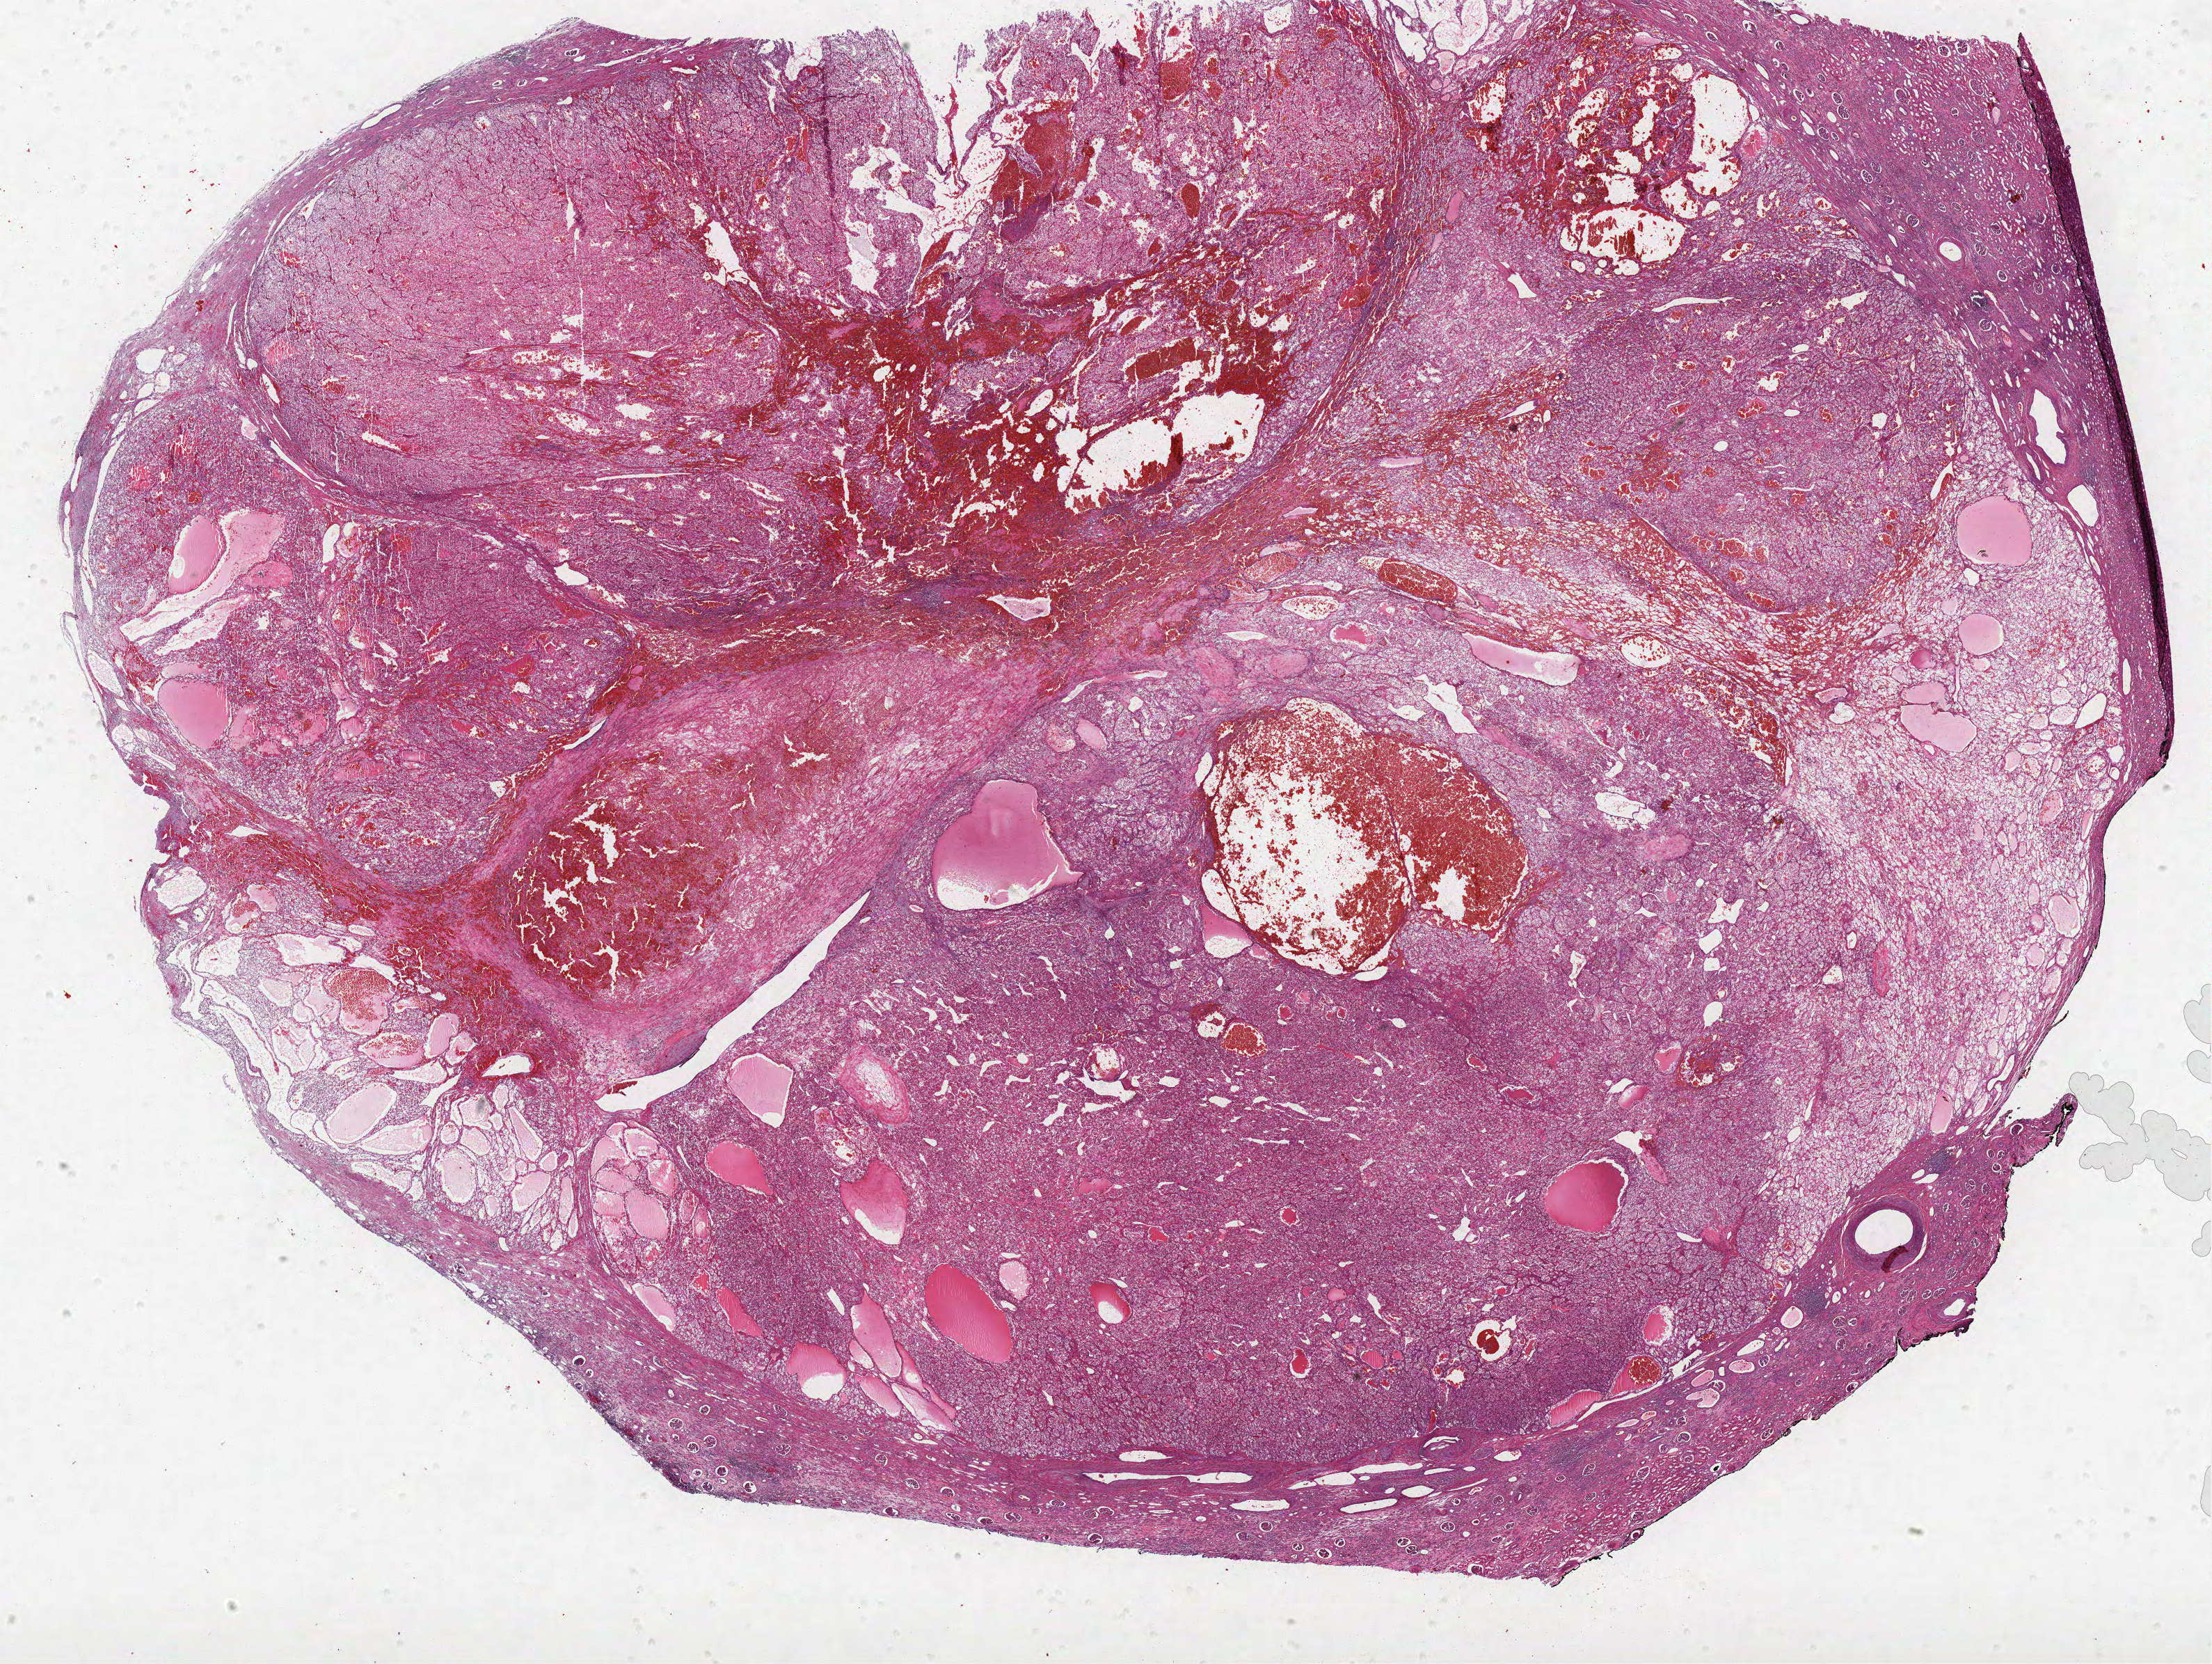
H&E-stained whole-slide image — low-resolution overview of the scanned area, about 25.4 x 19.1 mm, formalin-fixed paraffin-embedded (FFPE) diagnostic section, primary tumour sample from the kidney. Patient: male, age at initial diagnosis 75 years.
Pathologic diagnosis: Clear cell adenocarcinoma, NOS.